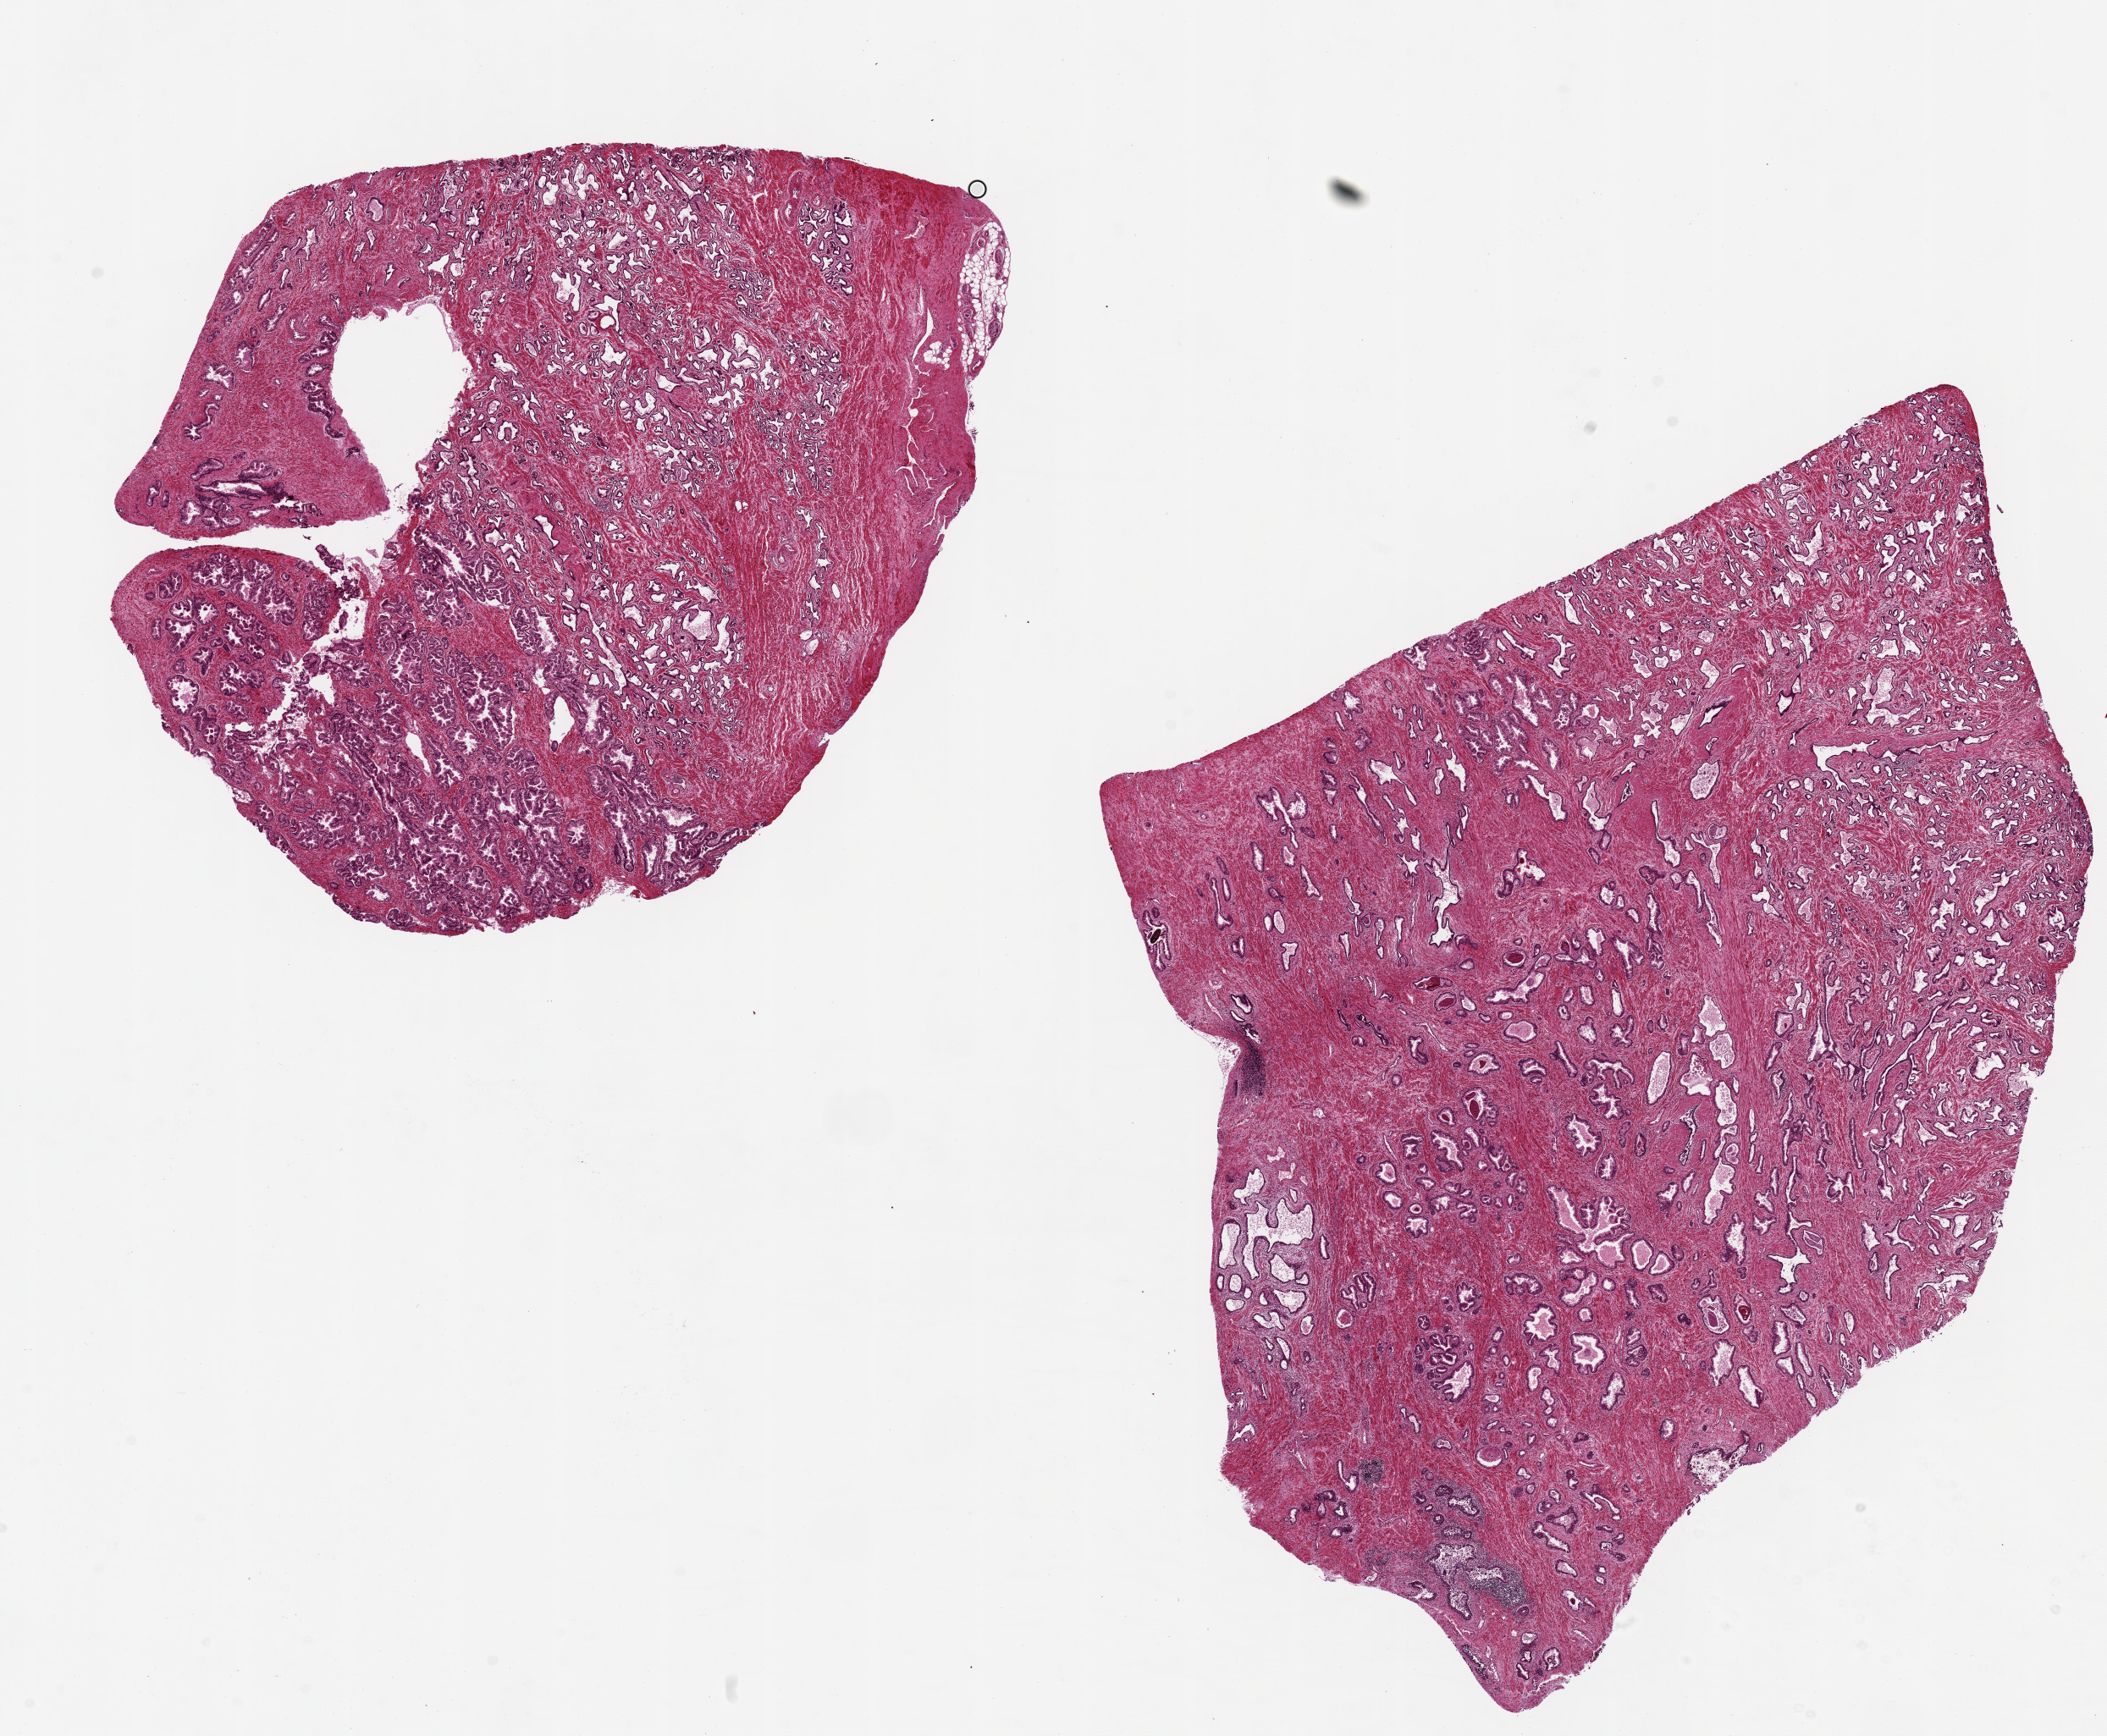
Digitized haematoxylin and eosin-stained section, brightfield — shown as a low-resolution overview of the whole scanned area (about 19.7 x 16.2 mm), PAXgene-fixed, paraffin-embedded tissue, section of prostate (target tissue), tissue donor sample. Donor: male.
Reviewer comment on this tissue sample: 2 aliquots, ~9x7mm. Diffuse glandular hyperplasia. Mucosa unusually well-preserved.